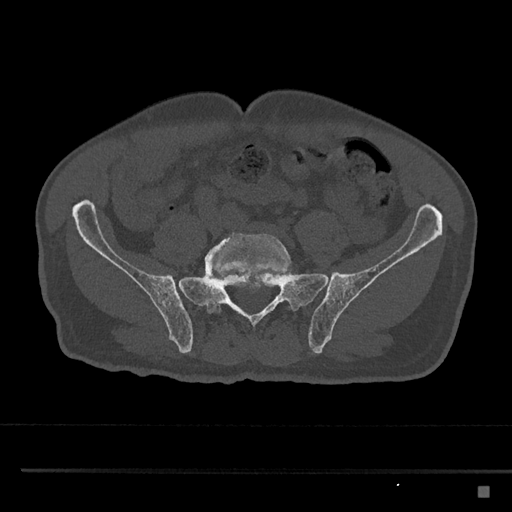
CT including the spine, one axial slice; slice 553 of 797 in the series (ordered by position); bone window (W 1800 / L 400 HU); 0.5 mm slice thickness; 512 × 512 image matrix, field of view 391 × 391 mm. Male patient, age 59 years. From the clinical record (not read from this slice): primary cancer: prostate.
Structures marked on this image (semi-automatically segmented with operator editing):
- L5 vertebra: bounding box (x1, y1, x2, y2) in pixels: (204, 232, 293, 313)